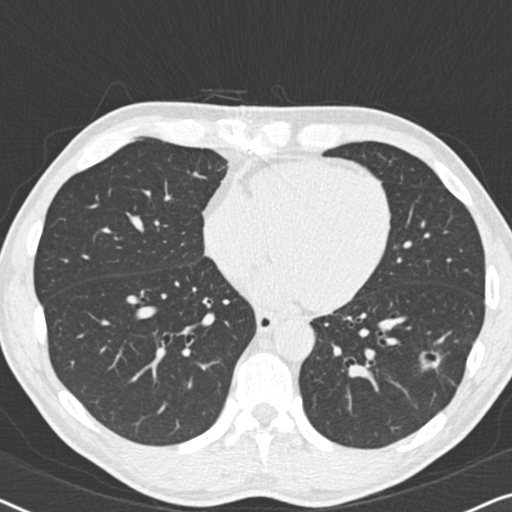
Low-dose screening chest CT, axial slice, second screening round (one year after baseline), lung window (W 1500 / L -600 HU), 2 mm slice thickness, standard (soft-tissue) reconstruction kernel (B30f), 120 kVp, 512 × 512 image matrix, field of view 330 × 330 mm. Male participant, aged 59 years at enrolment. Current smoker at enrolment.
Expert-annotated lung lesion, bounding box <413,337,461,381> (left, top, right, bottom; pixels). The screening reader recorded 2 non-calcified nodules or masses ≥4 mm on this exam; which of them this box marks is not recorded. Official screen result: positive, other. Participant outcome: lung cancer diagnosed 484 days after this screen — adenocarcinoma, NOS, left lower lobe, poorly differentiated (G3), stage IA (AJCC 6th edition), 20 mm at pathology.